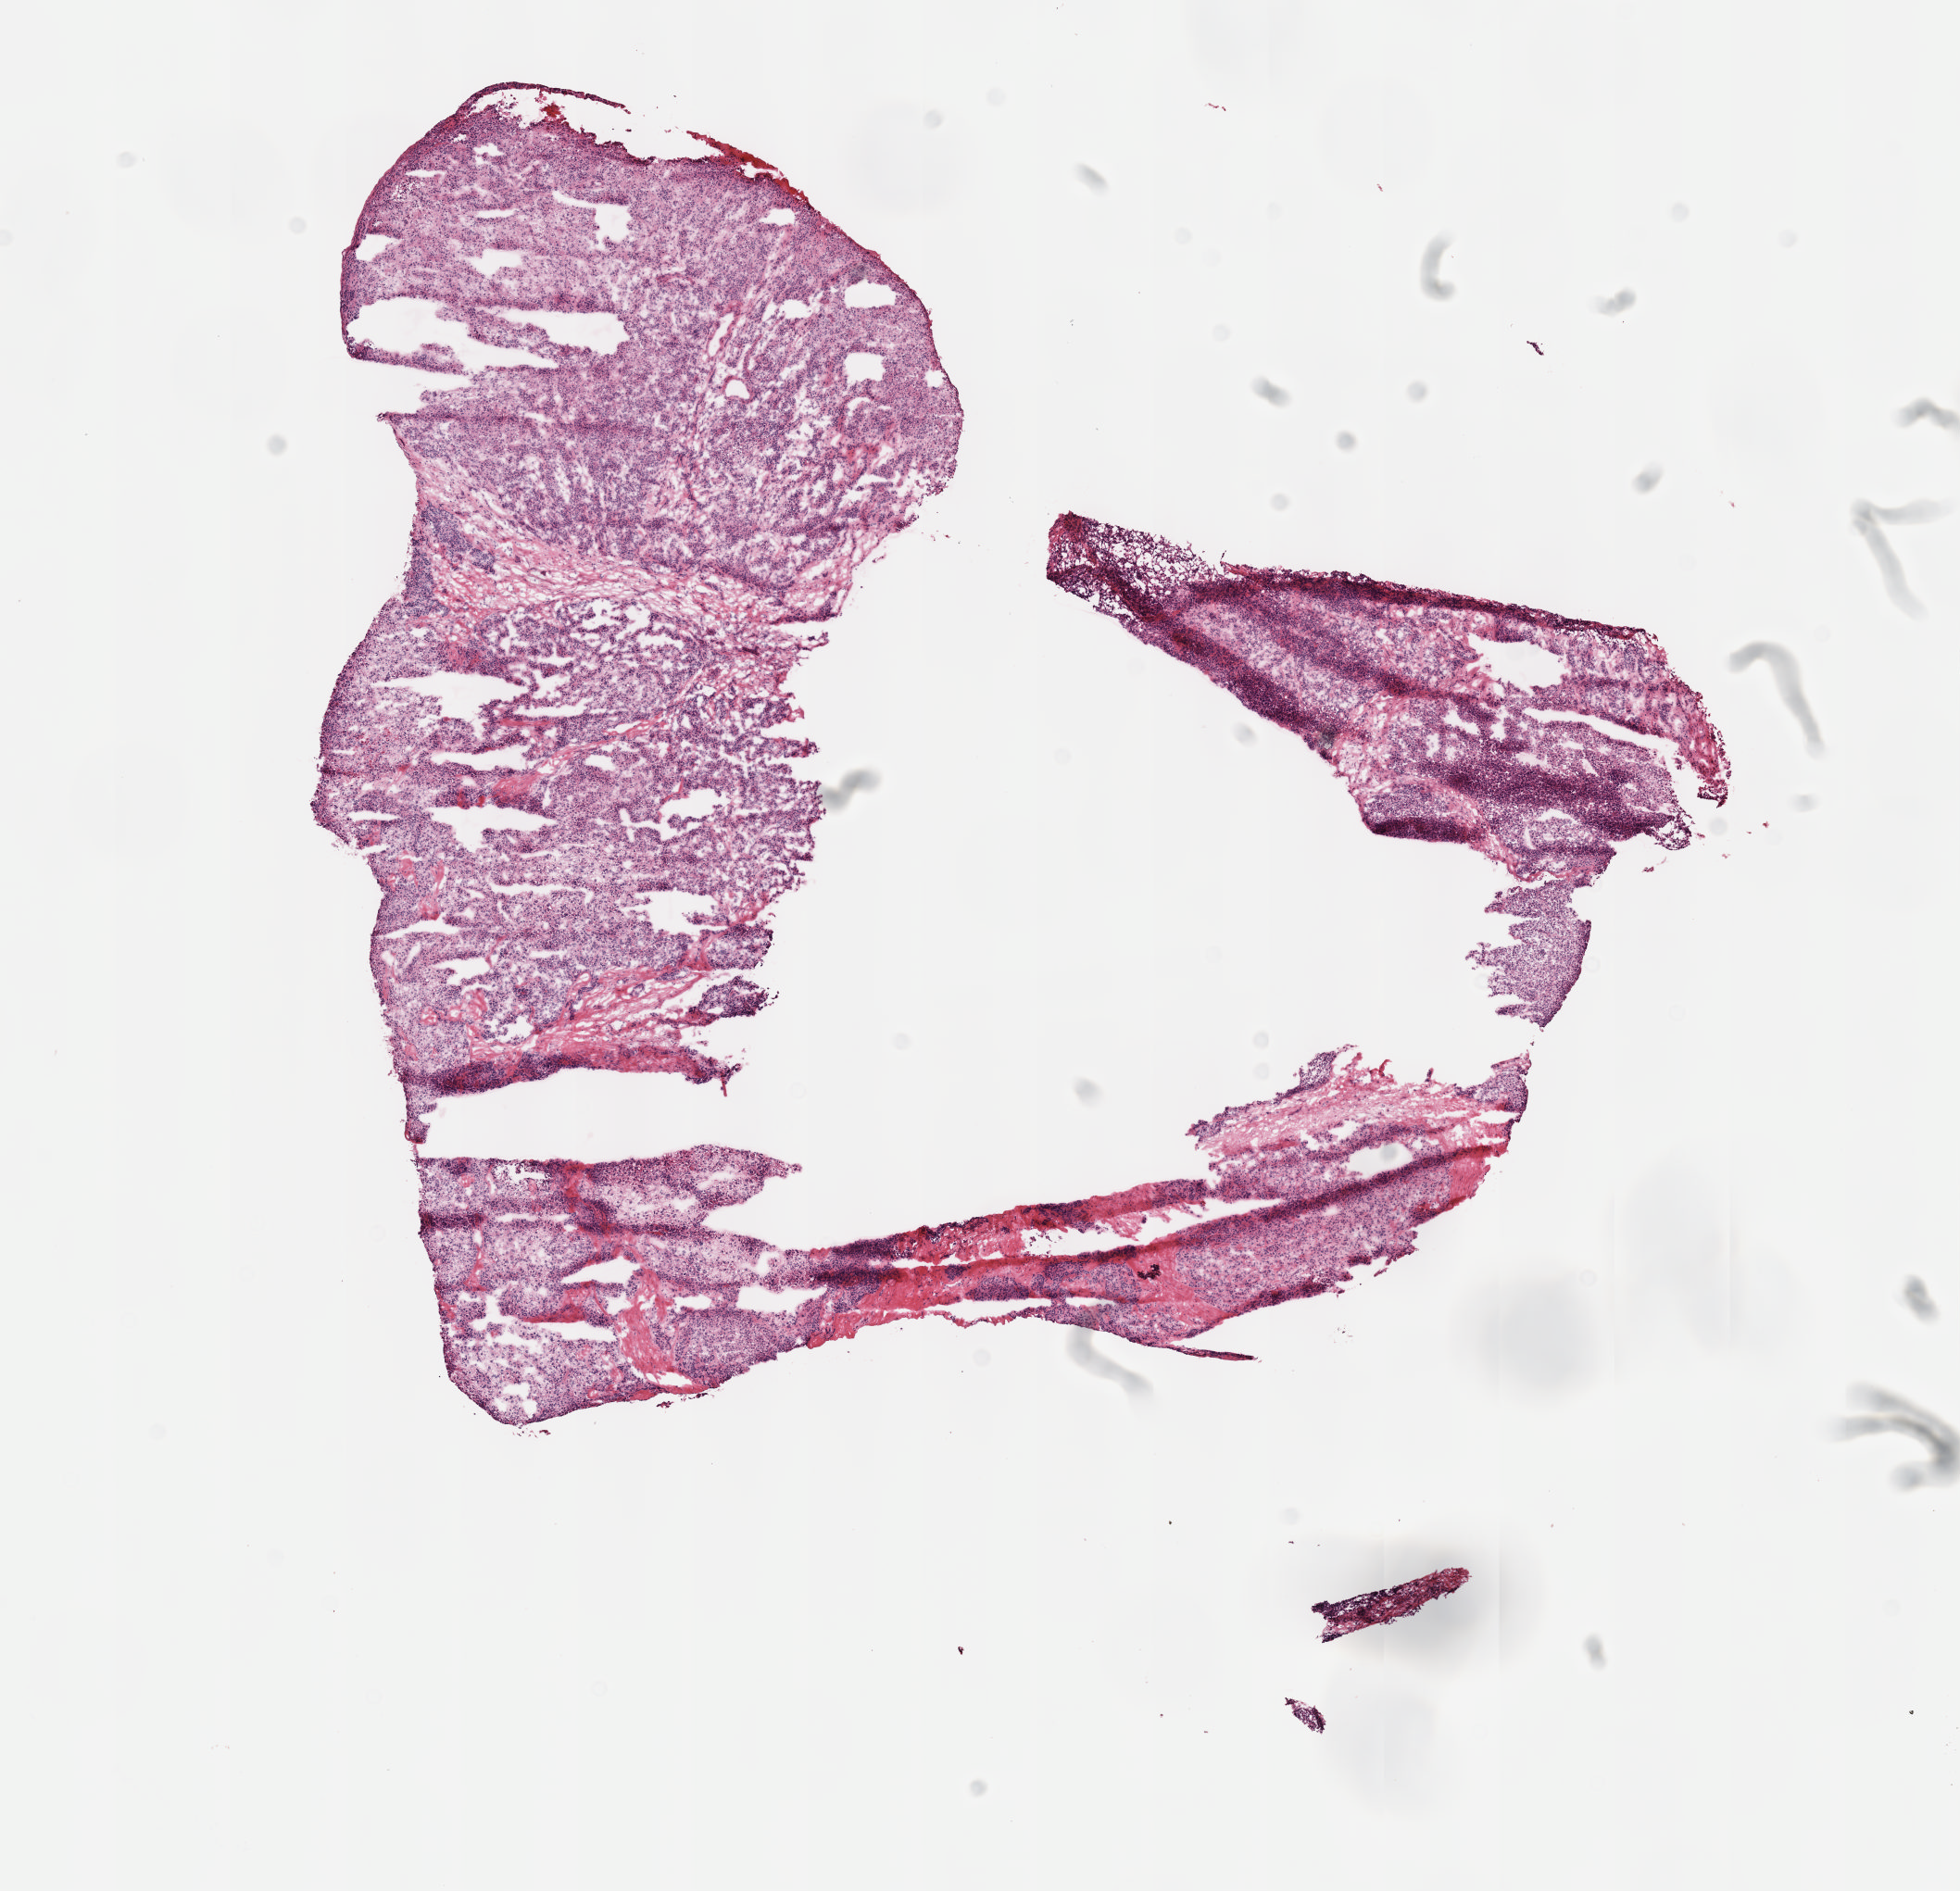
Digitized Hematoxylin and eosin (H&E) stained tissue section (whole slide), low-resolution overview of the scanned area, about 8.6 x 8.3 mm (acquisition: 40x scan); frozen section from the top of the tissue portion; liver, primary tumour sample. Patient: male, age at initial diagnosis 48 years.
Histologic diagnosis: Hepatocellular carcinoma, NOS.